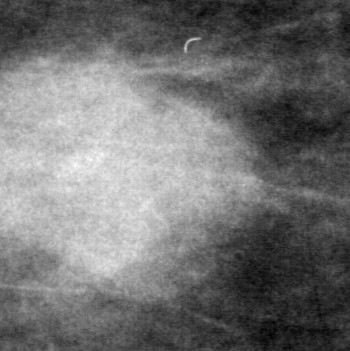
Cropped region of a digitized screen-film mammogram centred on a radiologist-marked abnormality, left breast, CC view.
Mass, shape oval, margins obscured; BI-RADS assessment category 0 (incomplete: needs additional imaging); pathology result (as recorded, not read from the image): benign.